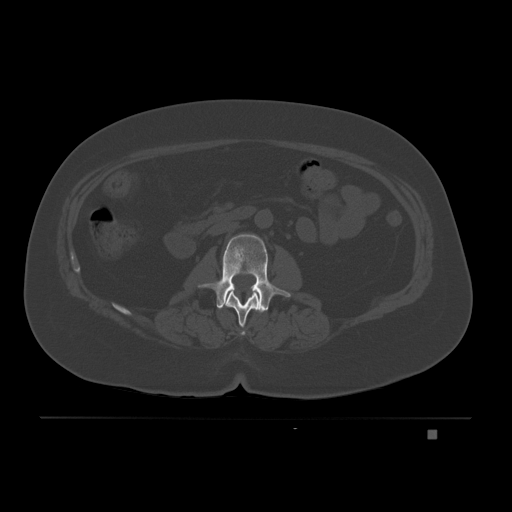
CT including the spine, one axial slice. Slice 64 of 221 in the series (ordered by position). Bone window (W 1800 / L 400 HU). 512 × 512 image matrix, field of view 474 × 474 mm. Female patient, age 63 years. From the clinical record (not read from this slice): primary cancer: breast.
Outlined on this slice (semi-automatic segmentation, software-assisted and operator-edited):
- L1 vertebra: bounding box <224,290,263,335> (left, top, right, bottom; pixels)
- L2 vertebra: <198,234,291,311>